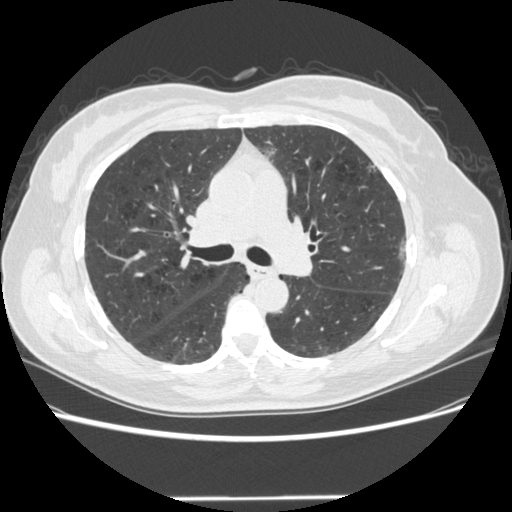
Chest CT (low-dose screening protocol), one axial image. Baseline annual screen. Lung window (W 1500 / L -600 HU). 1.25 mm slice thickness. 120 kVp. Slice 195 of 301 in the series. 512 × 512 image matrix. Female participant, aged 61 years at enrolment.
• Expert-annotated lung lesion, box from (x=381, y=226) to (x=425, y=278) px.
• No non-calcified nodule or mass ≥4 mm was recorded by the screening reader at this exam.
• Lung cancer was diagnosed 791 days after this screen (after the second annual screen): bronchiolo-alveolar adenocarcinoma, NOS, left upper lobe, well differentiated (G1), stage IA (AJCC 6th edition), 11 mm at pathology.